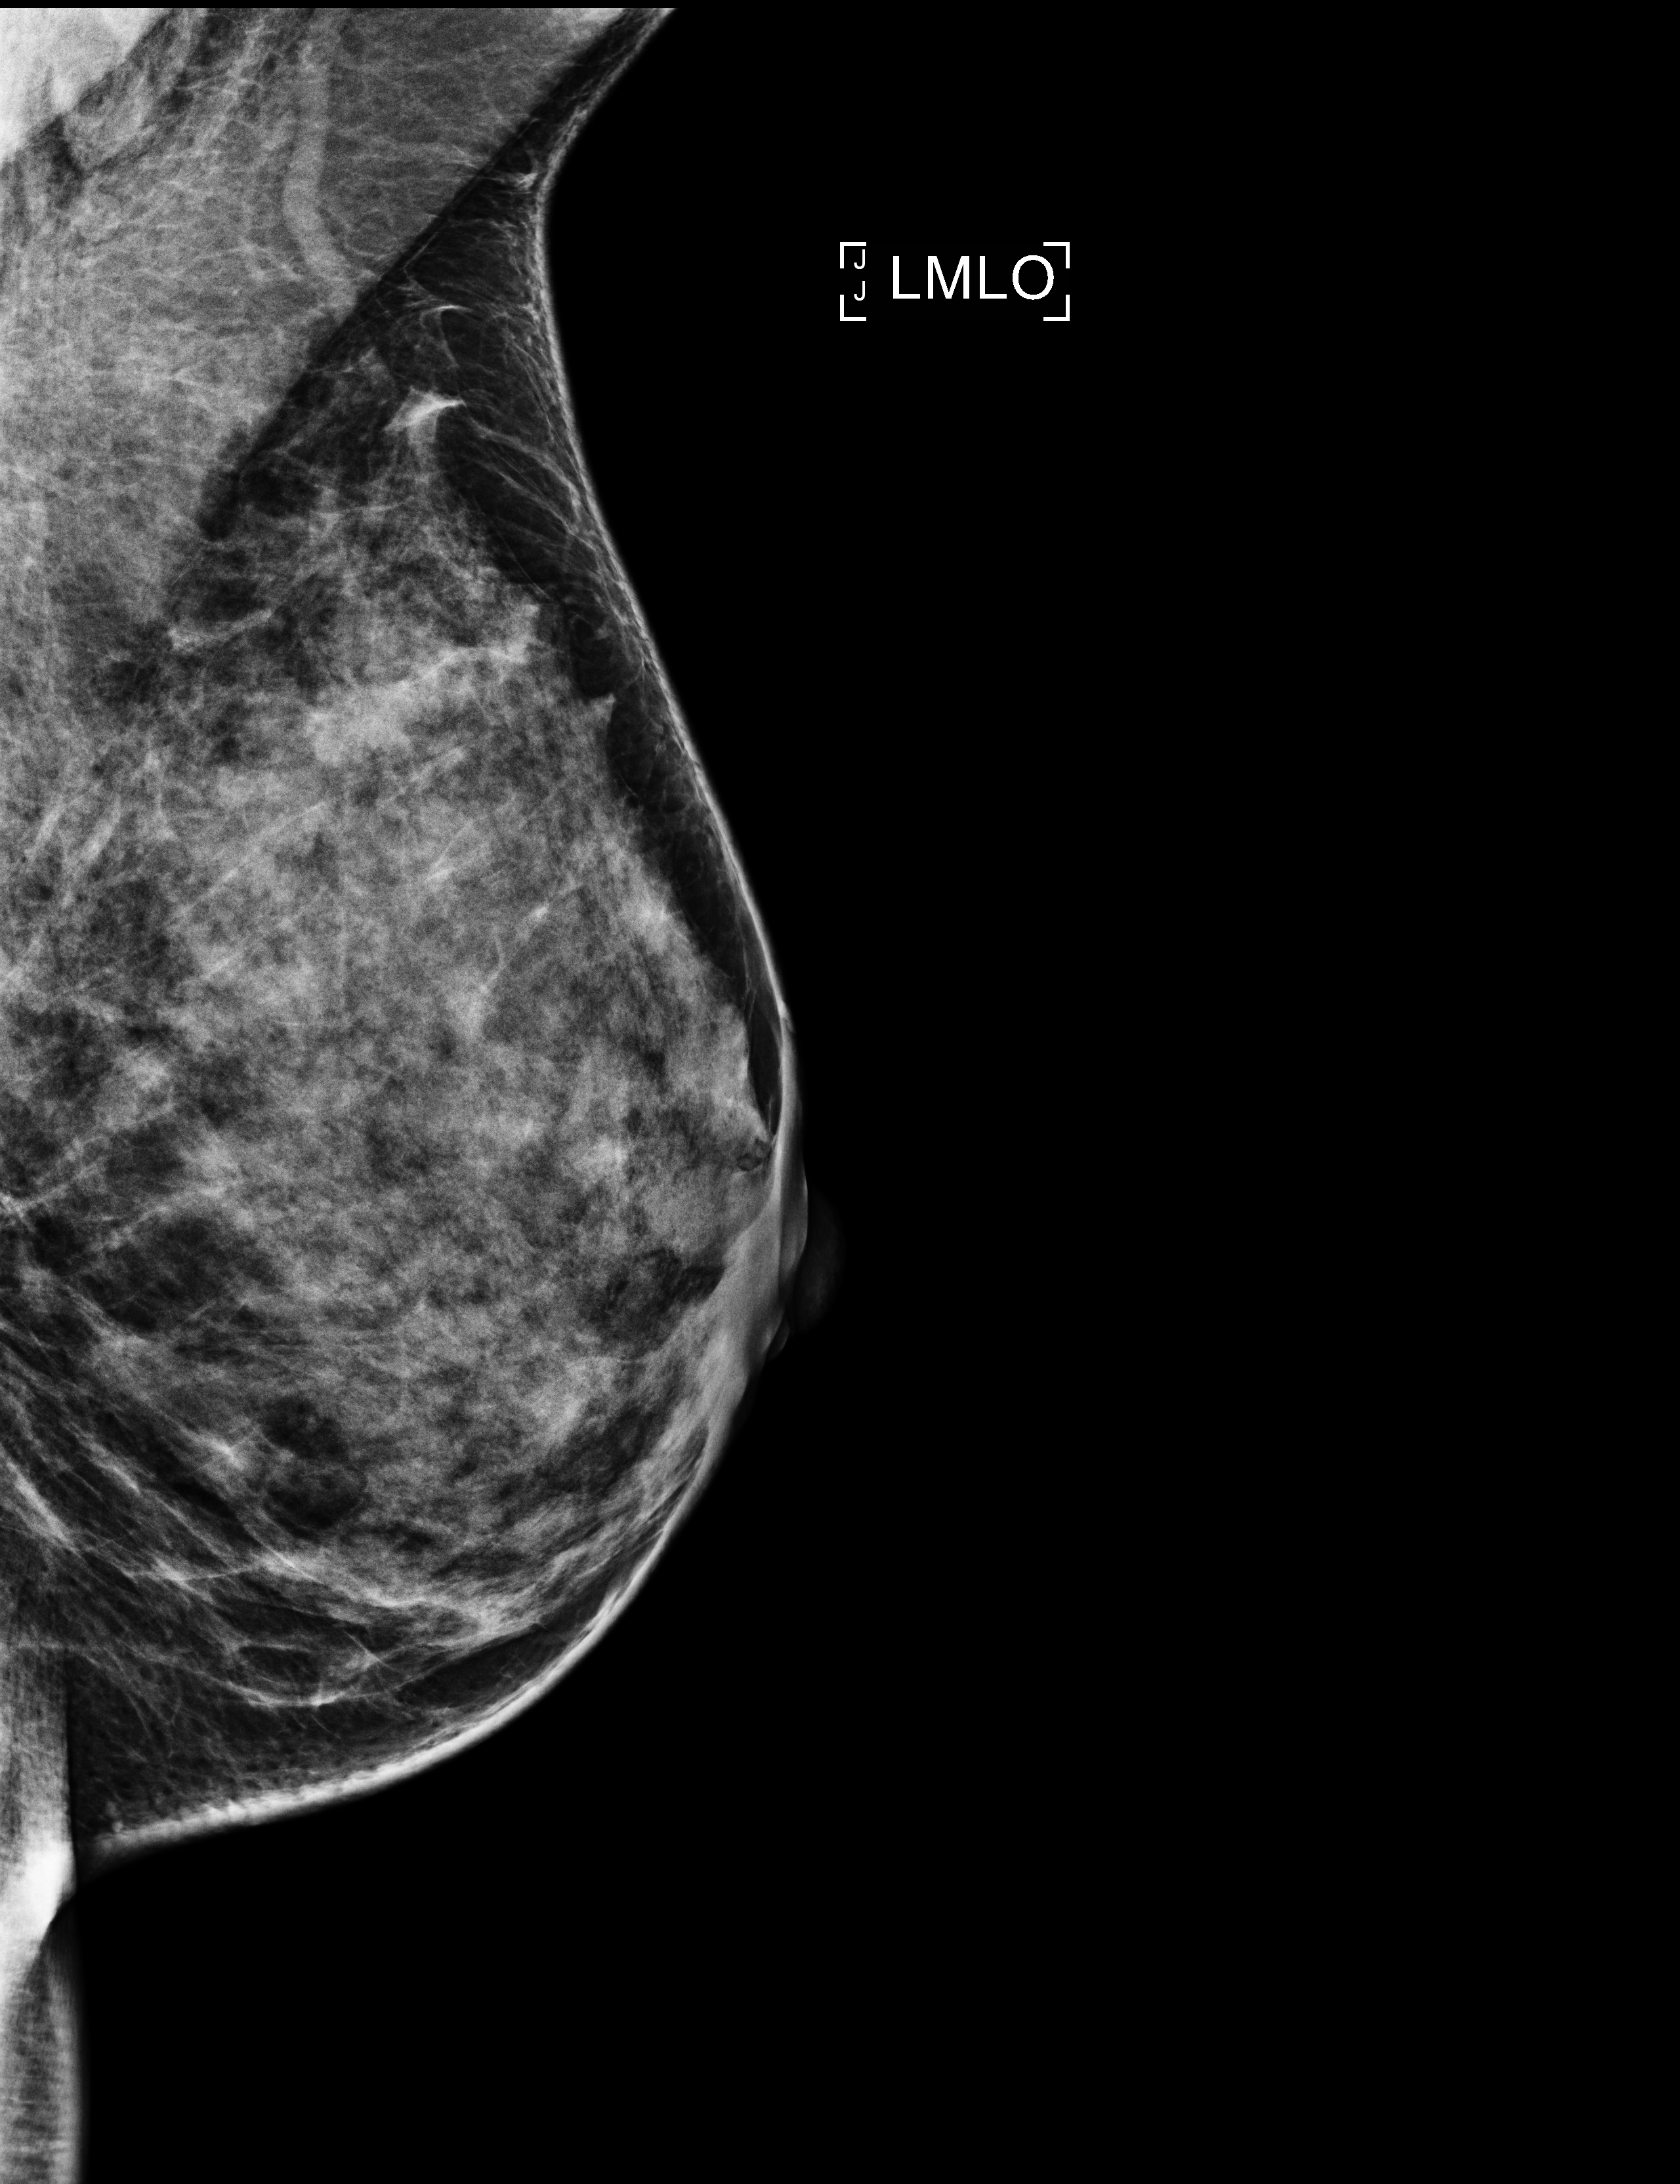
Full-field digital mammogram (FFDM); left breast; MLO view; annual screening mammography examination. Patient aged 43 years (female).
Breast density at the screening exam (both breasts): extremely dense (BI-RADS density category d). Final BI-RADS assessment for this screening round (tomosynthesis exam, both breasts): category 1. Recall: no recall after this screen.